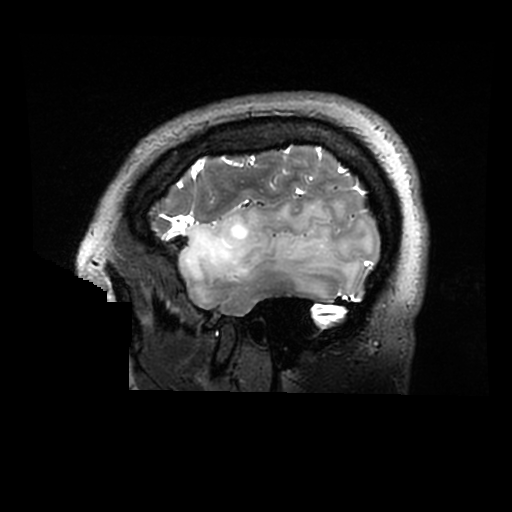
Brain MRI from a brain-tumour surgery series, one sagittal slice. Slice 241 of 320 in the series (ordered by position). 512 × 512 image matrix. Case-level facts recorded for this patient, not image findings: histopathology: Astrocytoma; WHO grade: 2; IDH mutation: yes.
Outlined on this slice (outlined manually by an expert reader):
- tumour: bounding box [x1, y1, x2, y2] px = [178, 201, 366, 299]